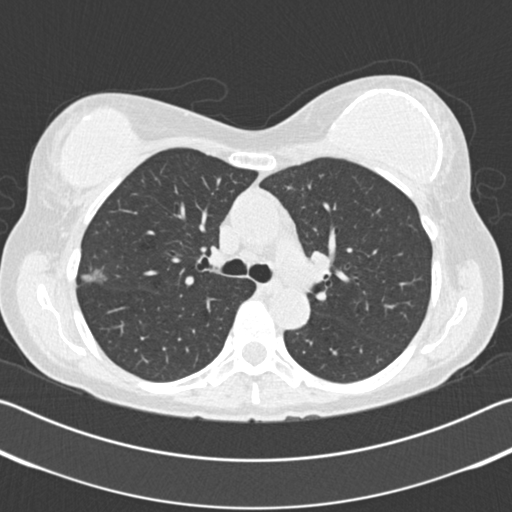
Low-dose screening chest CT, one axial slice; position 122 of 183 along the scan axis; reconstruction kernel B30f; 120 kVp; lung window (W 1500 / L -600 HU); 2 mm slice thickness; 512 × 512 image matrix.
Outlined on this slice (manually delineated by an expert):
- lesion 1 (tumor, upper lobe of right lung): bounding box (x1, y1, x2, y2) in pixels: (82, 269, 108, 284)